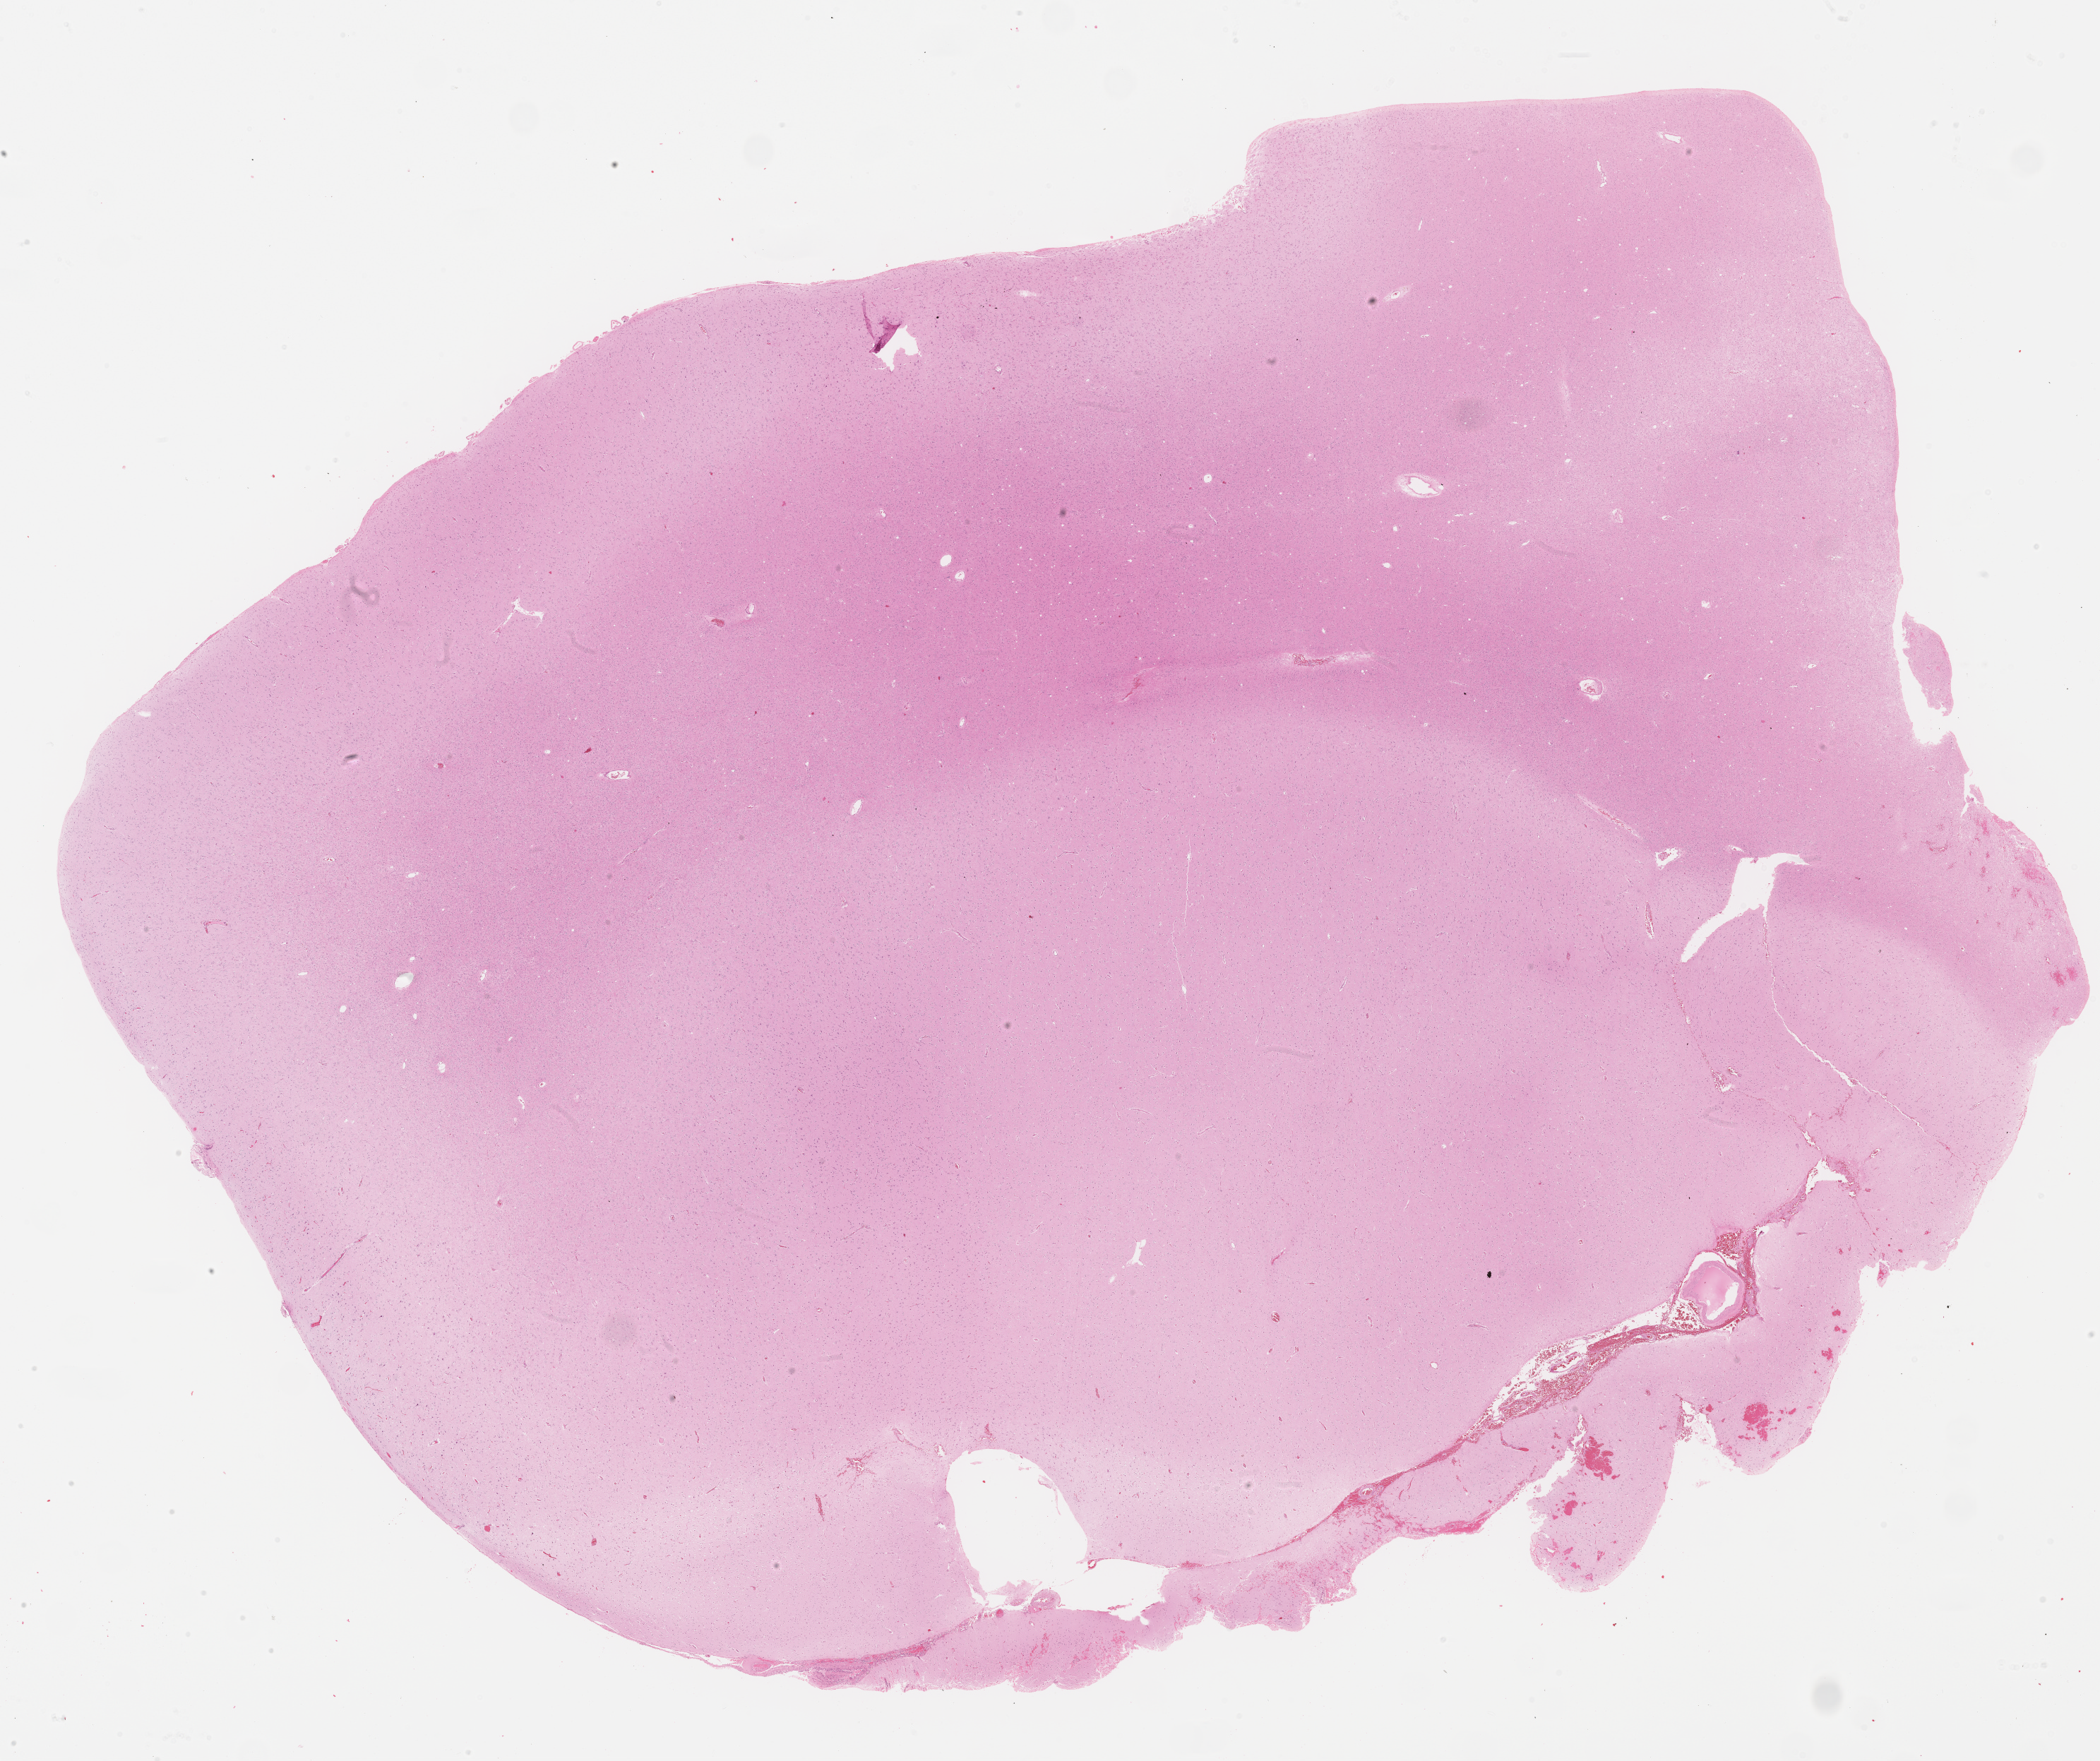
Digitized H&E-stained tissue section (whole slide) — shown as a low-resolution overview of the whole scanned area (about 24.0 x 20.1 mm, from a 40x scan). Formalin-fixed paraffin-embedded (FFPE) diagnostic section. Brain, primary tumour sample. Male patient; age at initial diagnosis 40 years. Histologic grade: G2 (moderately differentiated).
- histologic diagnosis: Oligodendroglioma, NOS (cerebrum)